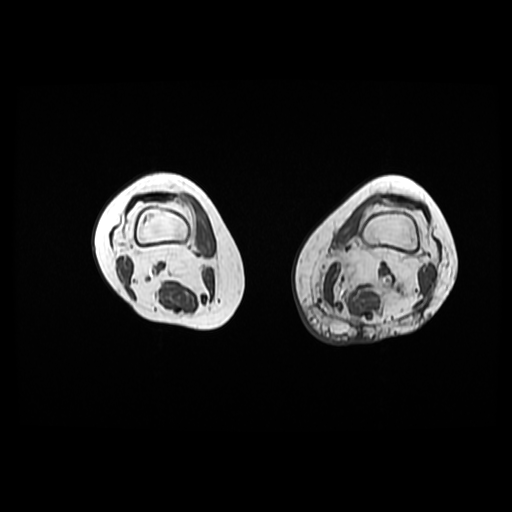
MRI of an extremity soft-tissue mass, one axial slice. Slice 14 of 42 in the series (ordered by position). 6 mm slice thickness. 512 × 512 image matrix, field of view 420 × 420 mm. Female patient. From the clinical record (not read from this slice): histological type: pleomorphic leiomyosarcoma; grade: high; site of the primary tumour: left thigh.
Annotated regions visible in this slice (expert manual segmentation):
- gross tumour volume including surrounding oedema: box from (x=313, y=262) to (x=346, y=315) px